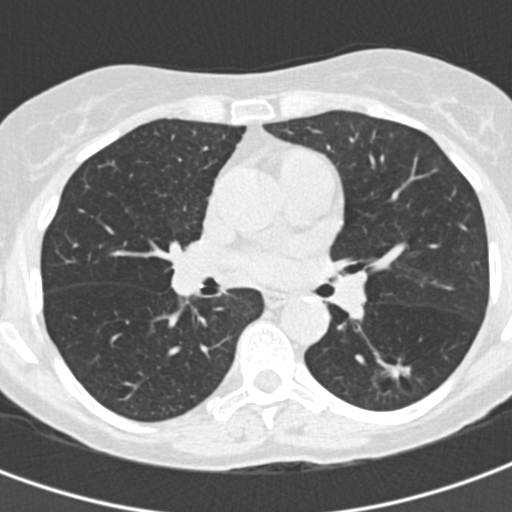
Low-dose screening chest CT, one axial slice; position 85 of 155 along the scan axis; lung window (W 1500 / L -600 HU); 2 mm slice thickness; 512 × 512 image matrix, field of view 282 × 282 mm.
Structures marked on this image (expert manual segmentation):
- lesion 1 (tumor, lower lobe of left lung): box from (x=381, y=362) to (x=411, y=382) px